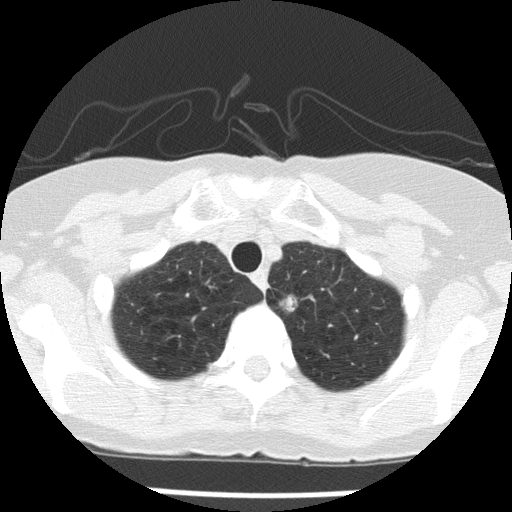
Low-dose screening chest CT, axial slice; baseline screening round; lung window (W 1500 / L -600 HU); 2 mm slice thickness; lung (sharp) reconstruction kernel (FC51); 120 kVp; slice 20 of 143 in the series. Female participant, aged 74 years at enrolment. Former smoker at enrolment.
Expert-annotated lung lesion, bounding box <271,289,307,317> (left, top, right, bottom; pixels). The screening reader recorded 2 non-calcified nodules or masses ≥4 mm on this exam (left lower lobe, left upper lobe); which of them this box marks is not recorded. Participant outcome: lung cancer diagnosed 81 days after this screen — adenocarcinoma, NOS, left upper lobe, poorly differentiated (G3), stage IA (AJCC 6th edition), 24 mm at pathology.